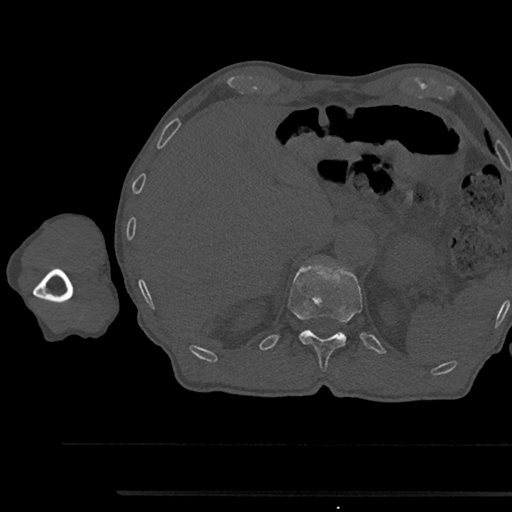
CT including the spine, one axial slice; slice 705 of 797 in the series (ordered by position); reconstruction kernel Br40s/3; bone window (W 1800 / L 400 HU); 0.5 mm slice thickness; 512 × 512 image matrix, field of view 367 × 367 mm. Patient: male, 79 years. Case-level facts recorded for this patient, not image findings: primary cancer: prostate.
Annotated regions visible in this slice (semi-automatic segmentation, software-assisted and operator-edited):
- T12 vertebra: bounding box [x1, y1, x2, y2] px = [288, 265, 362, 371]